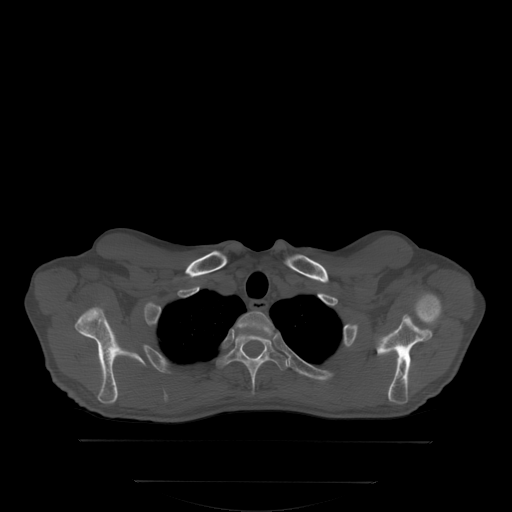
CT including the spine, one axial slice. Position 280 of 350 along the scan axis. Bone window (W 1800 / L 400 HU). 2.5 mm slice thickness. 512 × 512 image matrix. Patient: male, 58 years. From the clinical record (not read from this slice): primary cancer: prostate.
Structures marked on this image (semi-automatically segmented with operator editing):
- T1 vertebra: bounding box [x1, y1, x2, y2] px = [237, 311, 278, 338]
- T2 vertebra: [216, 330, 288, 386]
- T3 vertebra: [242, 352, 289, 366]